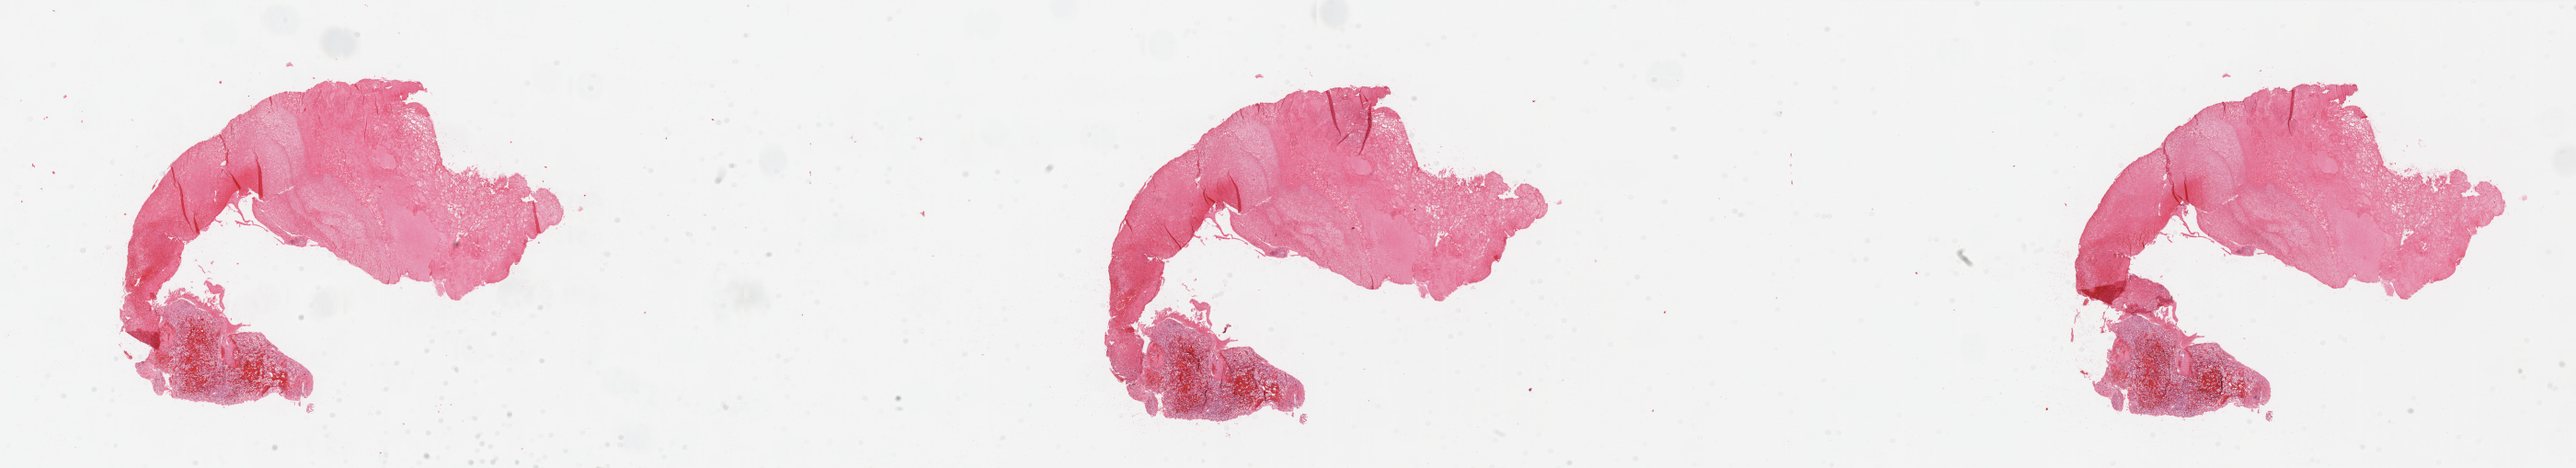
H&E whole-slide image — shown as a low-resolution overview of the whole scanned area (about 44.3 x 8.1 mm, from a 20x scan); tumour tissue sample, sampled site: kidney. Female, 51 y/o. Histologic grade: G3 (poorly differentiated). Slide review estimates, as recorded: tumour nuclei 80%, necrosis 70%.
- diagnosis: Renal cell carcinoma, NOS
- AJCC pathologic stage: IV